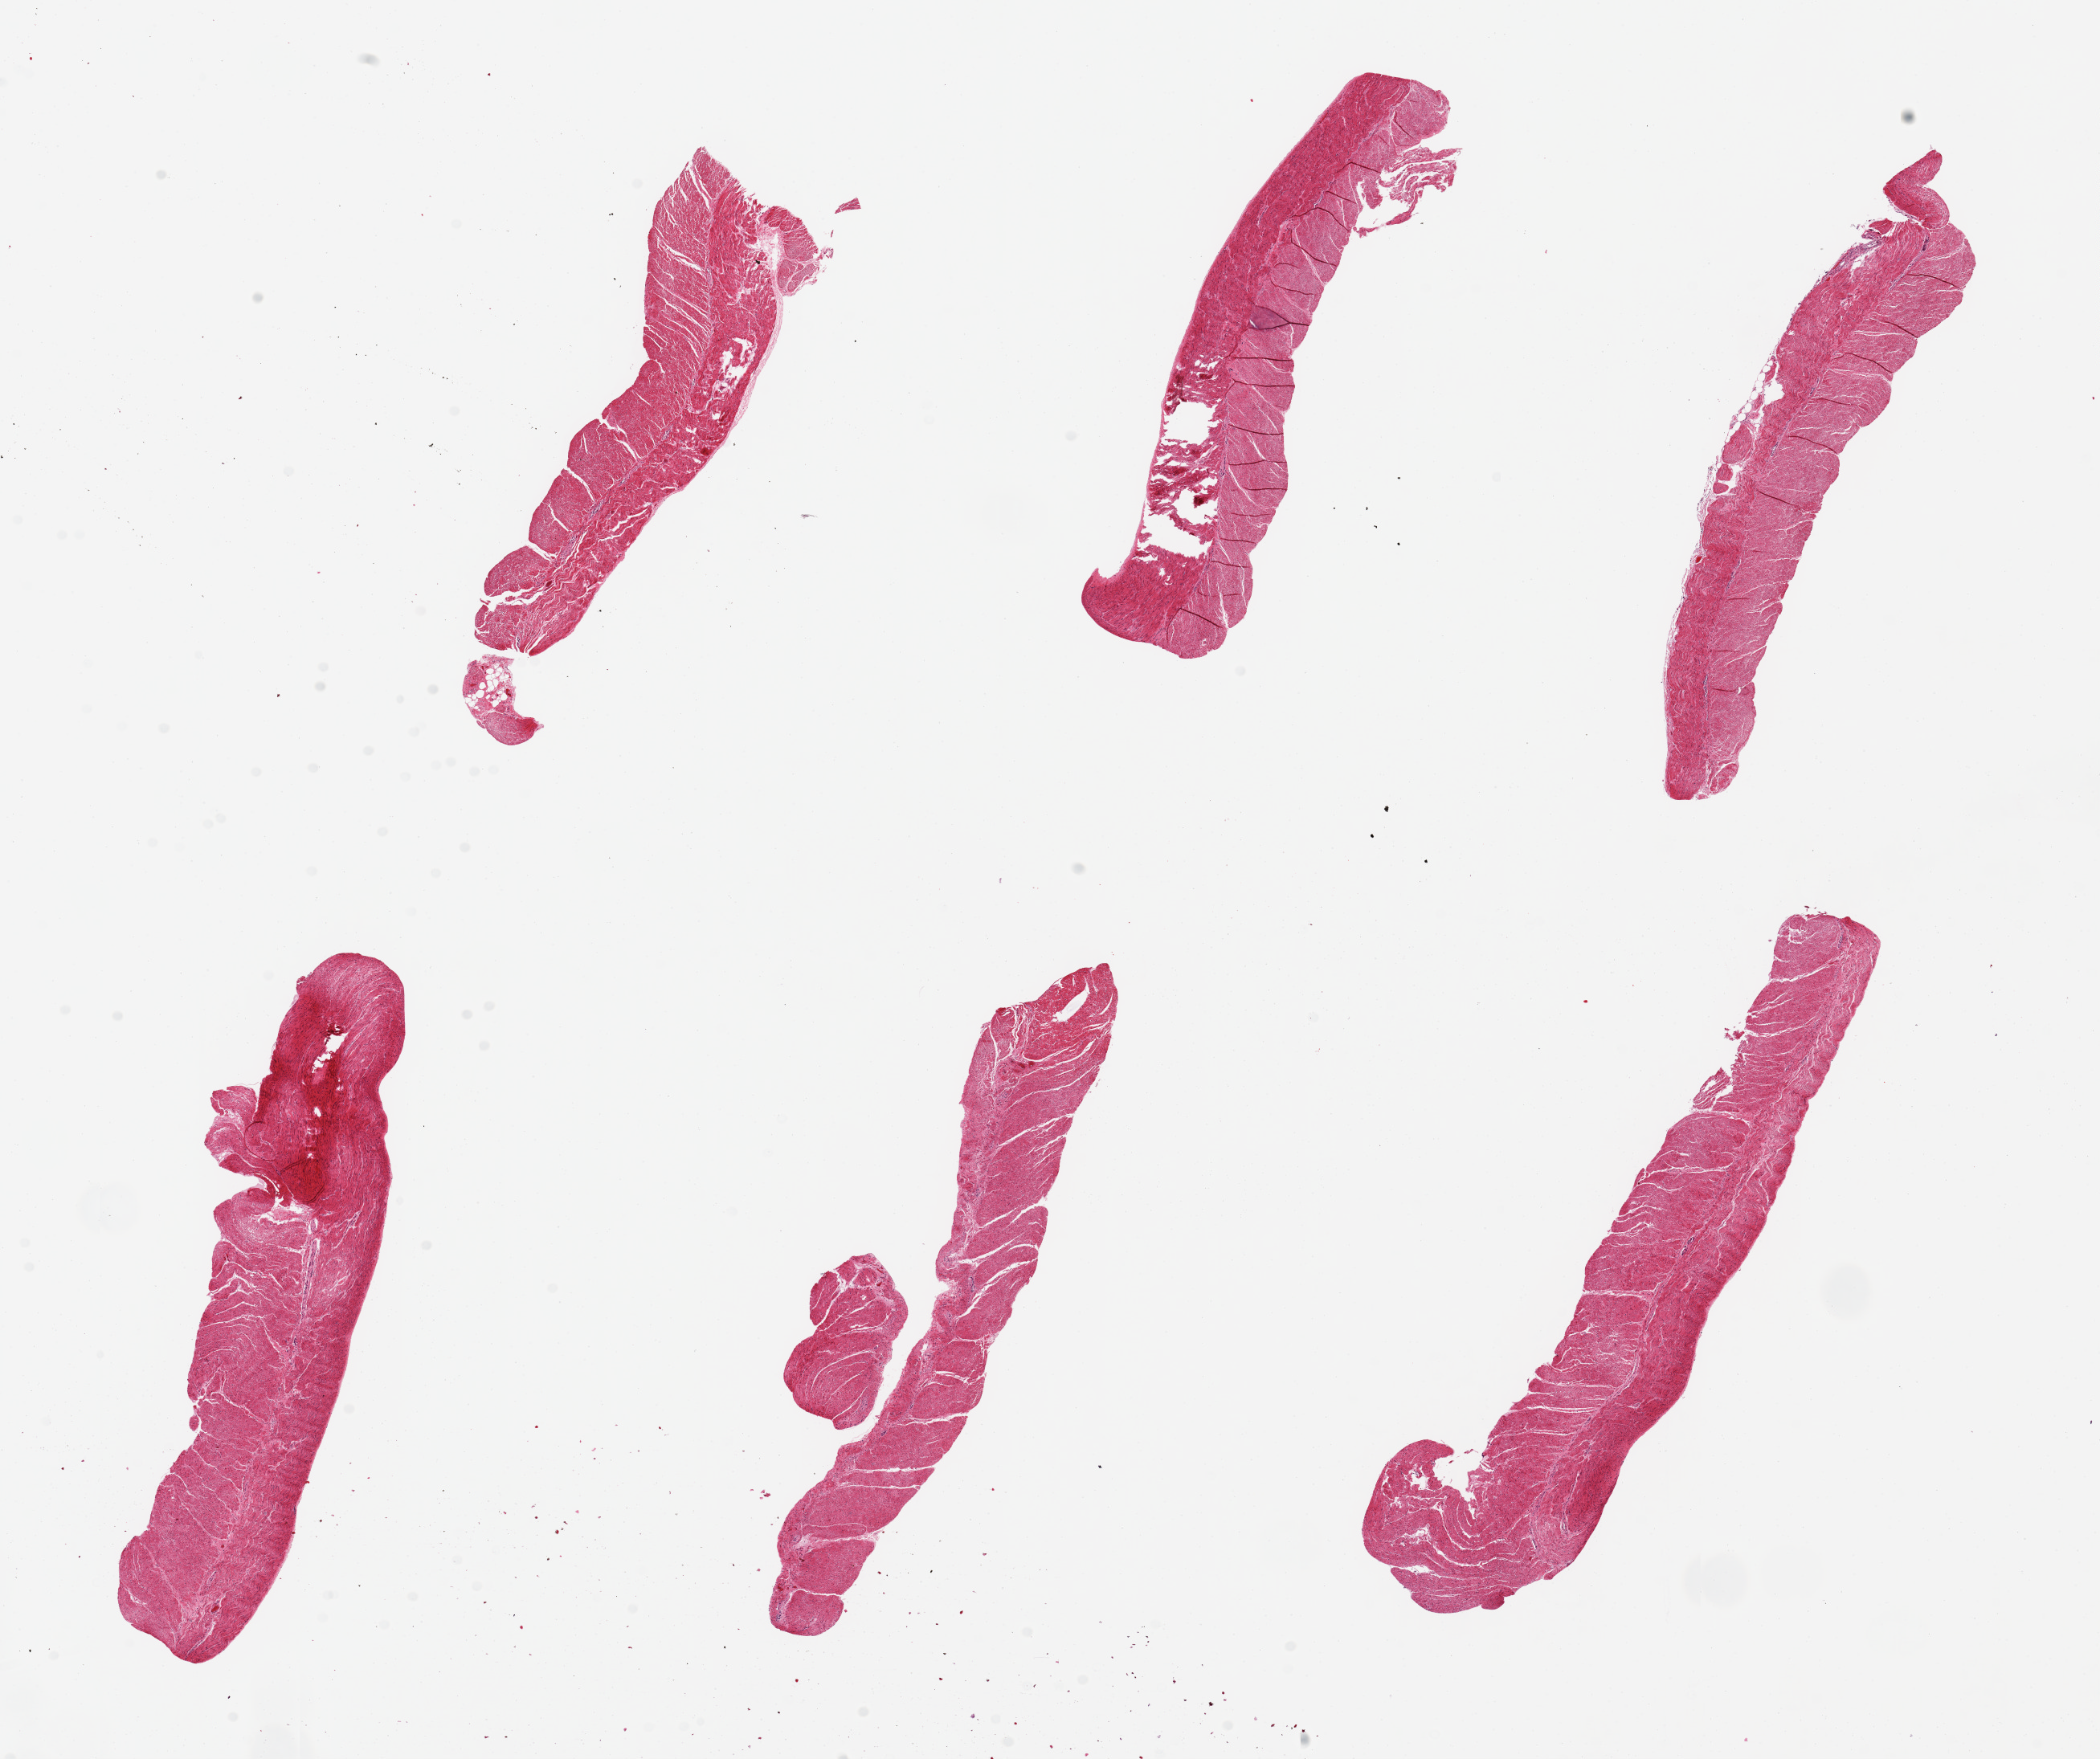
Digitized hematoxylin and eosin (H&E)-stained section, shown as a low-resolution overview of the whole scanned area (about 20.7 x 17.3 mm). PAXgene-fixed paraffin-embedded (PFPE) section. Sampled site (target tissue): sigmoid colon. Donor tissue sample.
Reviewer comment on this tissue sample: 6 pieces ~6x1mm, excllent specimens, all muscularis.